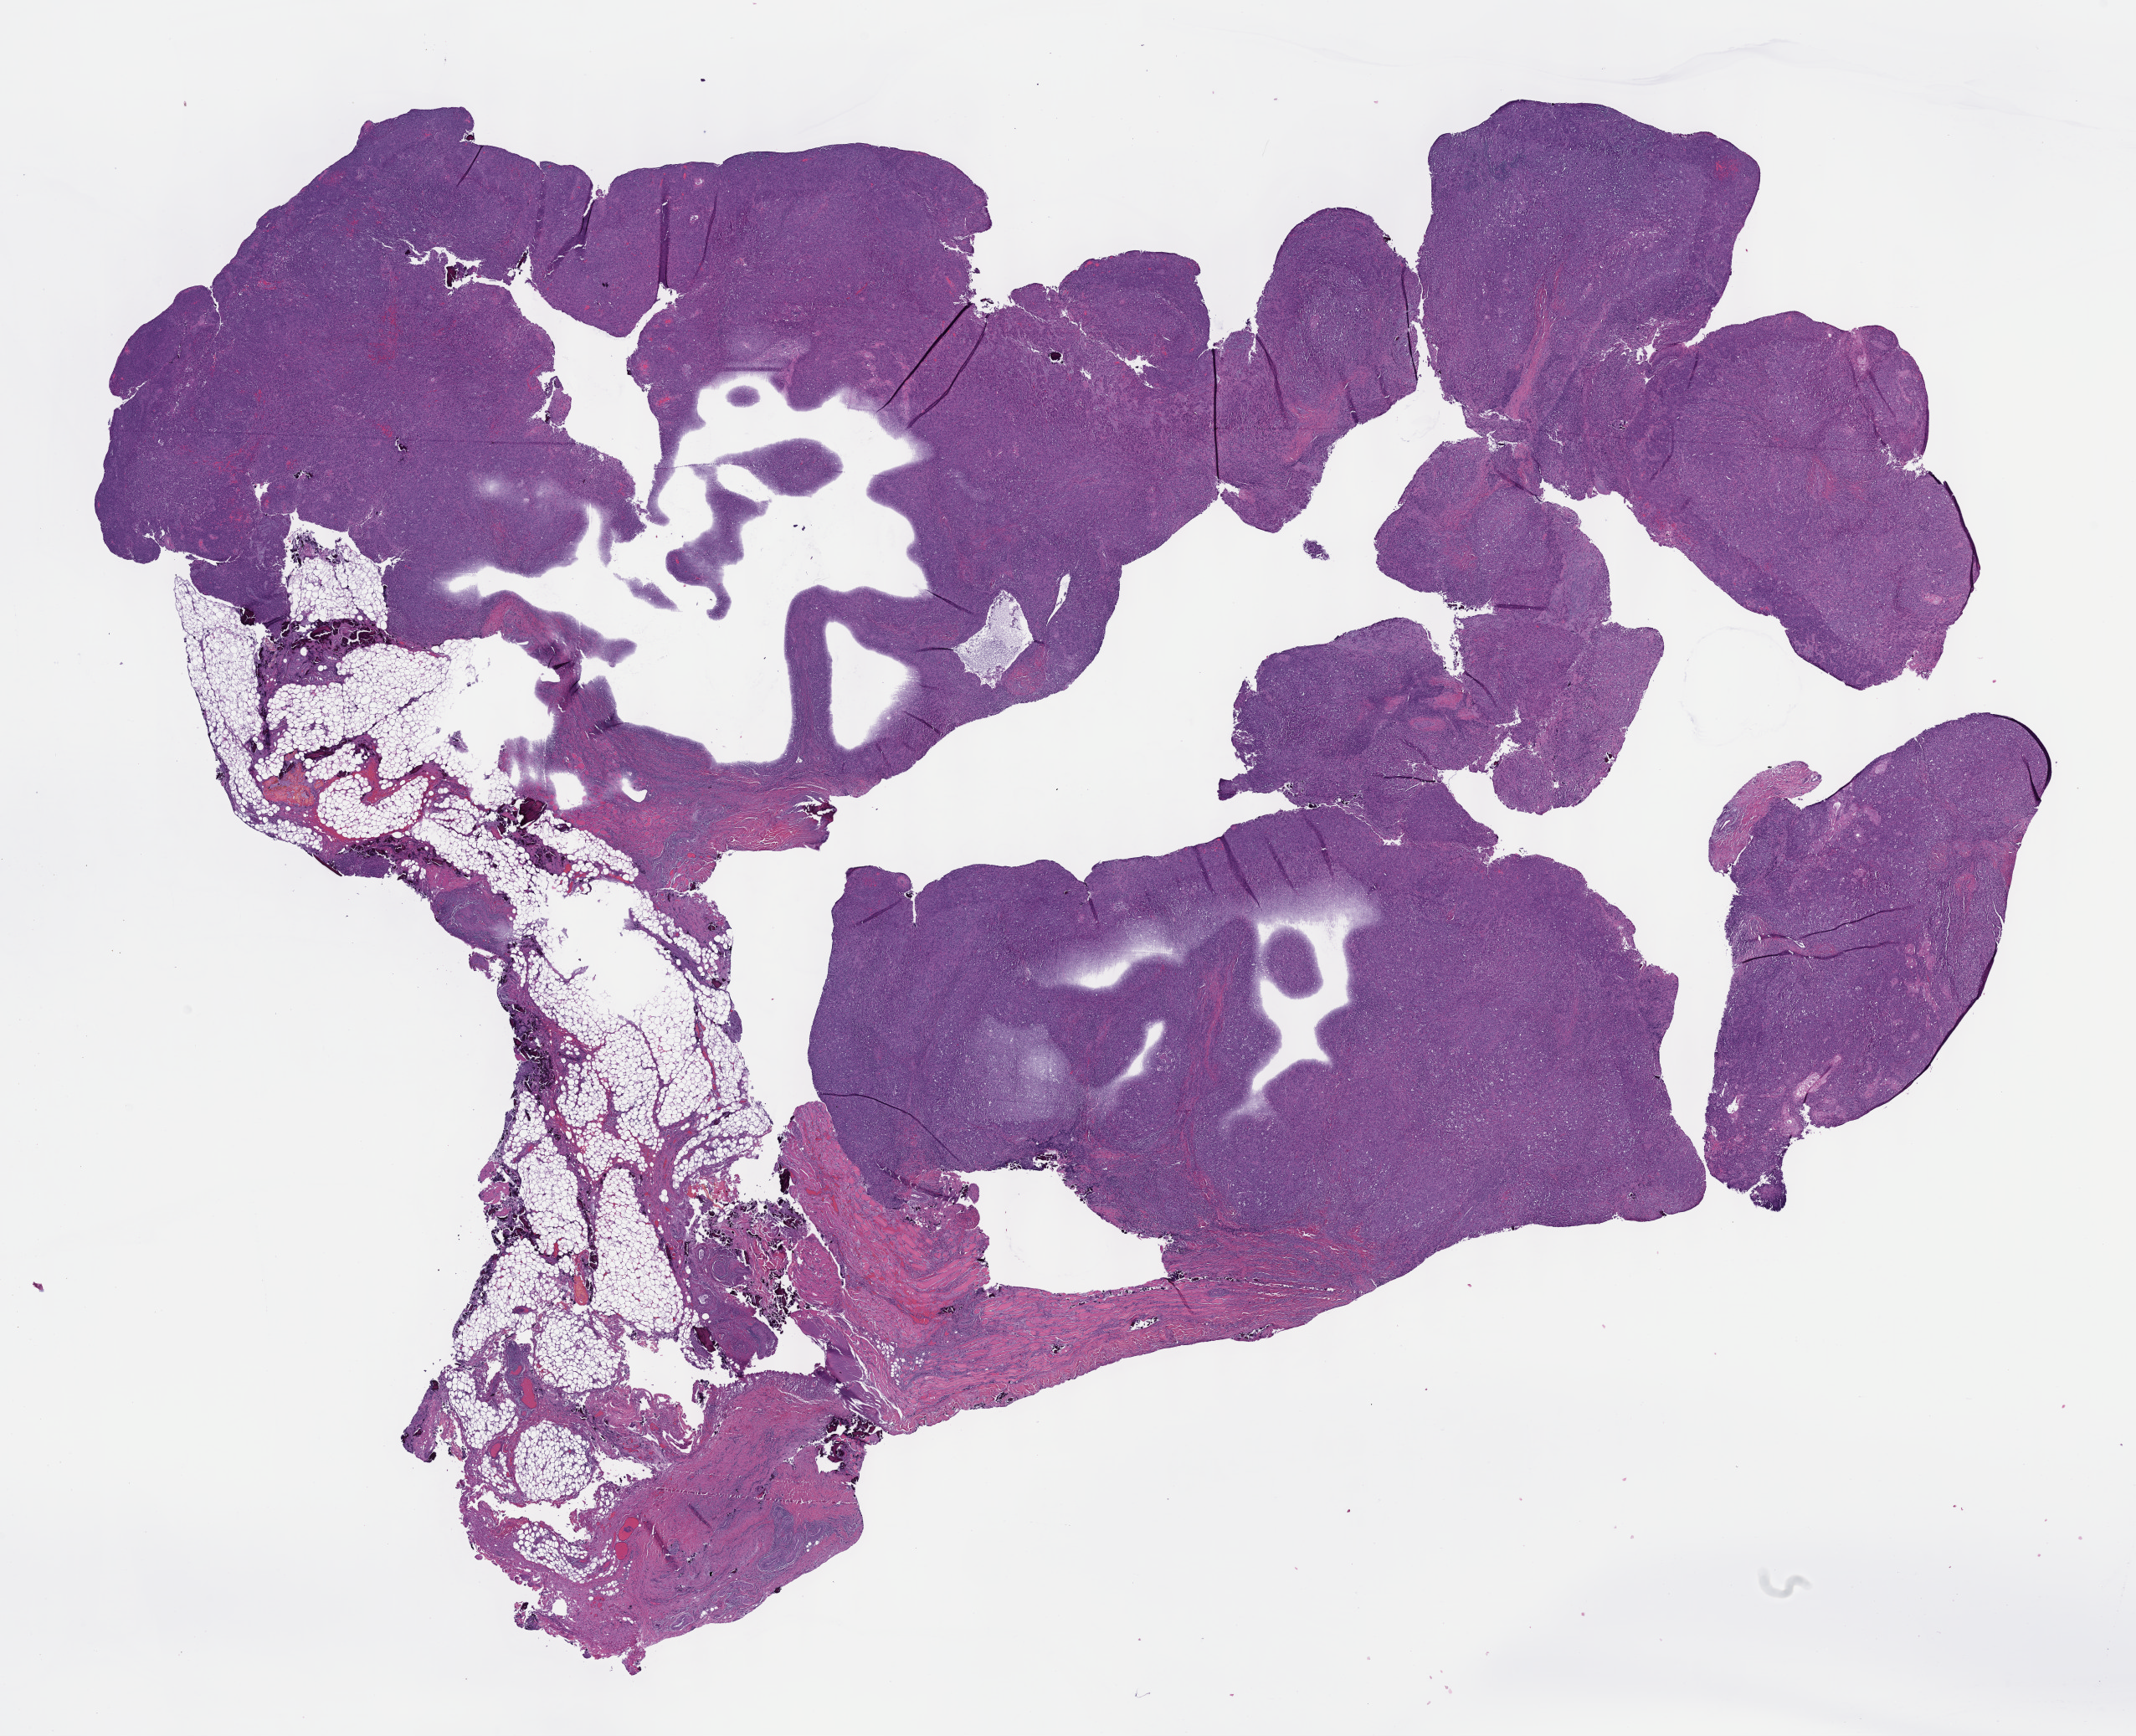
Digitized Hematoxylin and eosin (H&E) stained tissue section (whole slide), whole scanned area (about 20.6 x 16.8 mm) shown as a low-resolution overview, formalin-fixed paraffin-embedded (FFPE) diagnostic section, sample: primary tumour, head and neck. Female patient; age at initial diagnosis 82 years. Histologic grade: G3 (poorly differentiated).
Histologic diagnosis: Squamous cell carcinoma, NOS (floor of mouth, NOS). Lymph nodes positive (case pathology): 0 of 23 examined.